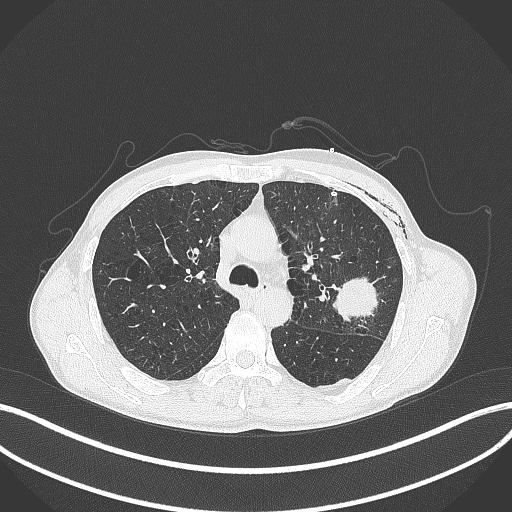
Chest CT, one axial slice. Position 273 of 457 along the scan axis. Lung window (W 1500 / L -600 HU). 1 mm slice thickness. 512 × 512 image matrix, field of view 400 × 400 mm. Patient: male, 58 years. Case-level facts recorded for this patient, not image findings: clinical TNM (as recorded): T3 N0 M0.
Structures marked on this image (rectangle marked by the reading radiologist):
- lung tumour (recorded histology: adenocarcinoma): bounding box (x1, y1, x2, y2) in pixels: (326, 269, 383, 330)